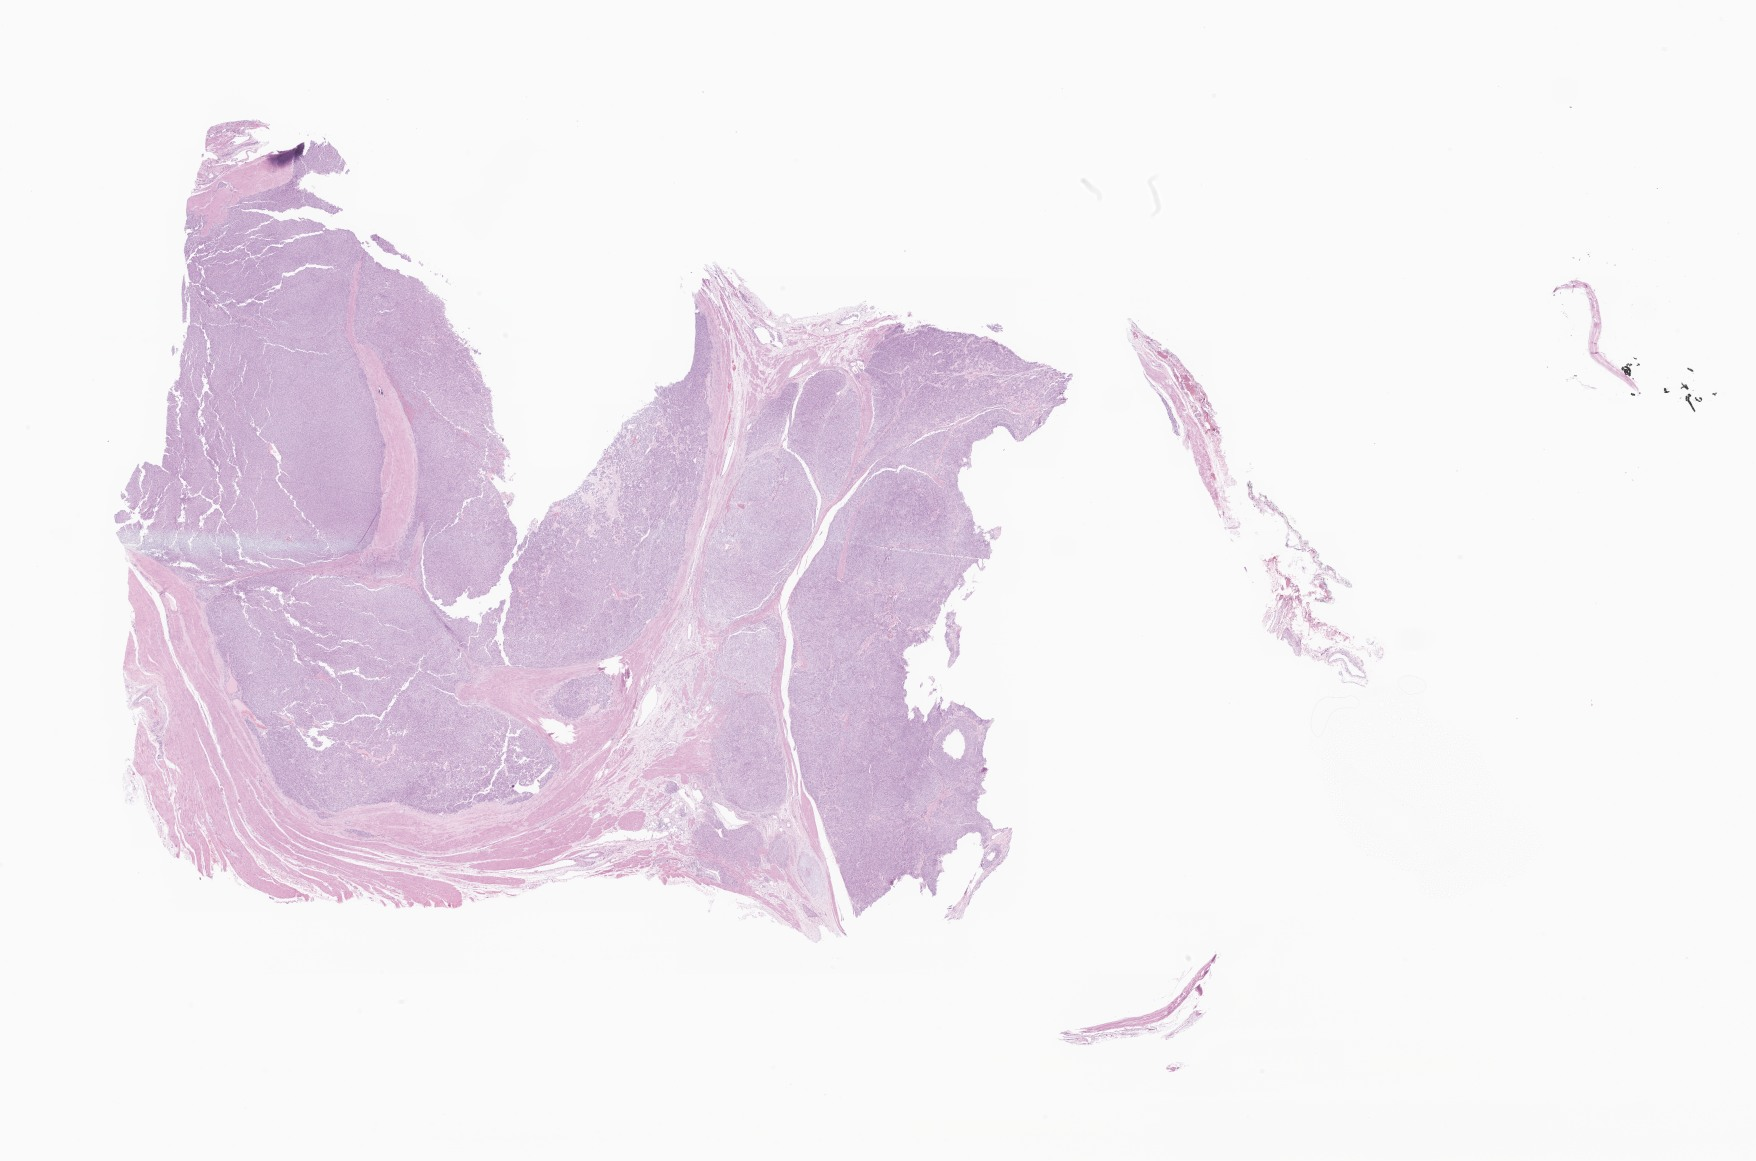
Digitized hematoxylin and eosin (H&E)-stained section of tumor tissue from the body of stomach, shown as a low-resolution overview of the whole scanned area (about 29.6 x 19.6 mm); formalin-fixed, paraffin-embedded (FFPE) tissue. Patient: female, age 147 months (12 years 3 months).
• diagnosis: Gastrointestinal stromal tumor, benign